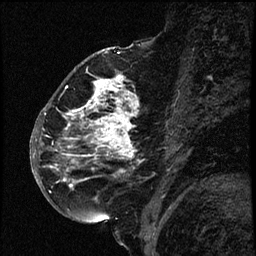
Breast MRI (dynamic contrast-enhanced), one sagittal slice; position 32 of 66 along the scan axis; dynamic contrast-enhanced study with each time point stored as its own series, time point 2 of 3 at this slice position (early post-contrast, ordered by acquisition time); 1.5 T; TE 4.2 ms, TR 17.6 ms; 2 mm slice thickness; 256 × 256 image matrix, field of view 200 × 200 mm. Female patient. Case-level facts recorded for this patient, not image findings: setting: breast cancer imaged before/during neoadjuvant chemotherapy; receptor status: HER2-positive.
Structures marked on this image (semi-automatically segmented with operator editing):
- analysis volume of interest (the breast-tissue region the enhancement analysis was run in; not a lesion): bounding box (x1, y1, x2, y2) in pixels: (52, 69, 155, 209)
- tumour enhancement mask (voxels above the 100 % enhancement threshold inside the analysis volume of interest): (54, 75, 140, 189)